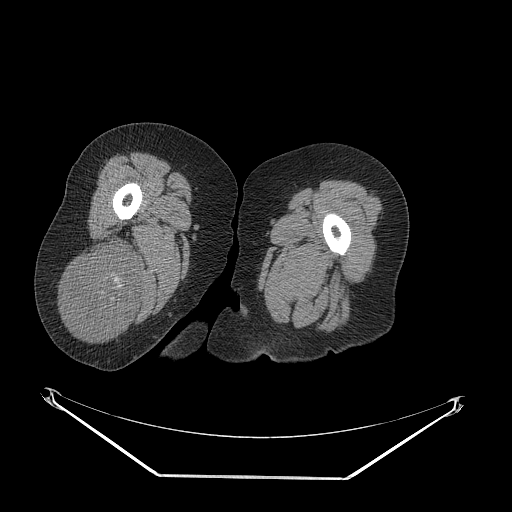
CT of an extremity soft-tissue mass (from a PET/CT study), one axial slice. Slice 37 of 257 in the series (ordered by position). 140 kVp. Soft-tissue window (W 400 / L 40 HU). 3.75 mm slice thickness. 512 × 512 image matrix. Female patient. From the clinical record (not read from this slice): histological type: synovial sarcoma; grade: intermediate; site of the primary tumour: right buttock.
Structures marked on this image (expert contour drawn on MRI and transferred to this co-registered scan by the dataset authors):
- gross tumour volume including surrounding oedema: box from (x=64, y=240) to (x=143, y=337) px
- gross tumour volume (mass): (x=64, y=247)–(x=143, y=337)